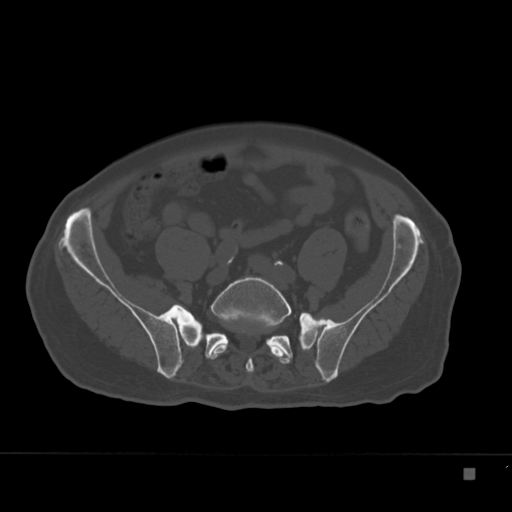
CT including the spine, one axial slice. Position 15 of 332 along the scan axis. Reconstruction kernel Br40s. 120 kVp. Bone window (W 1800 / L 400 HU). 512 × 512 image matrix, field of view 389 × 389 mm. Male patient, age 72 years. Case-level facts recorded for this patient, not image findings: primary cancer: skeletal.
Annotated regions visible in this slice (semi-automatically segmented with operator editing):
- L5 vertebra: box from (x=206, y=276) to (x=292, y=373) px